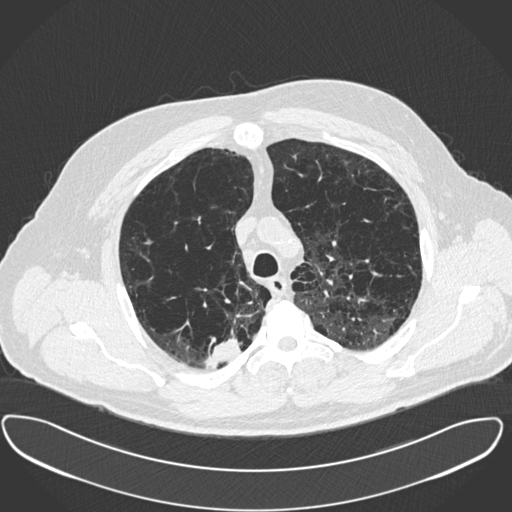
Low-dose screening chest CT, one axial slice; position 299 of 385 along the scan axis; reconstruction kernel B30f; 120 kVp; lung window (W 1500 / L -600 HU); 512 × 512 image matrix, field of view 408 × 408 mm.
Structures marked on this image (outlined manually by an expert reader):
- lesion 1 (tumor, upper lobe of right lung): bounding box (x1, y1, x2, y2) in pixels: (204, 339, 241, 369)